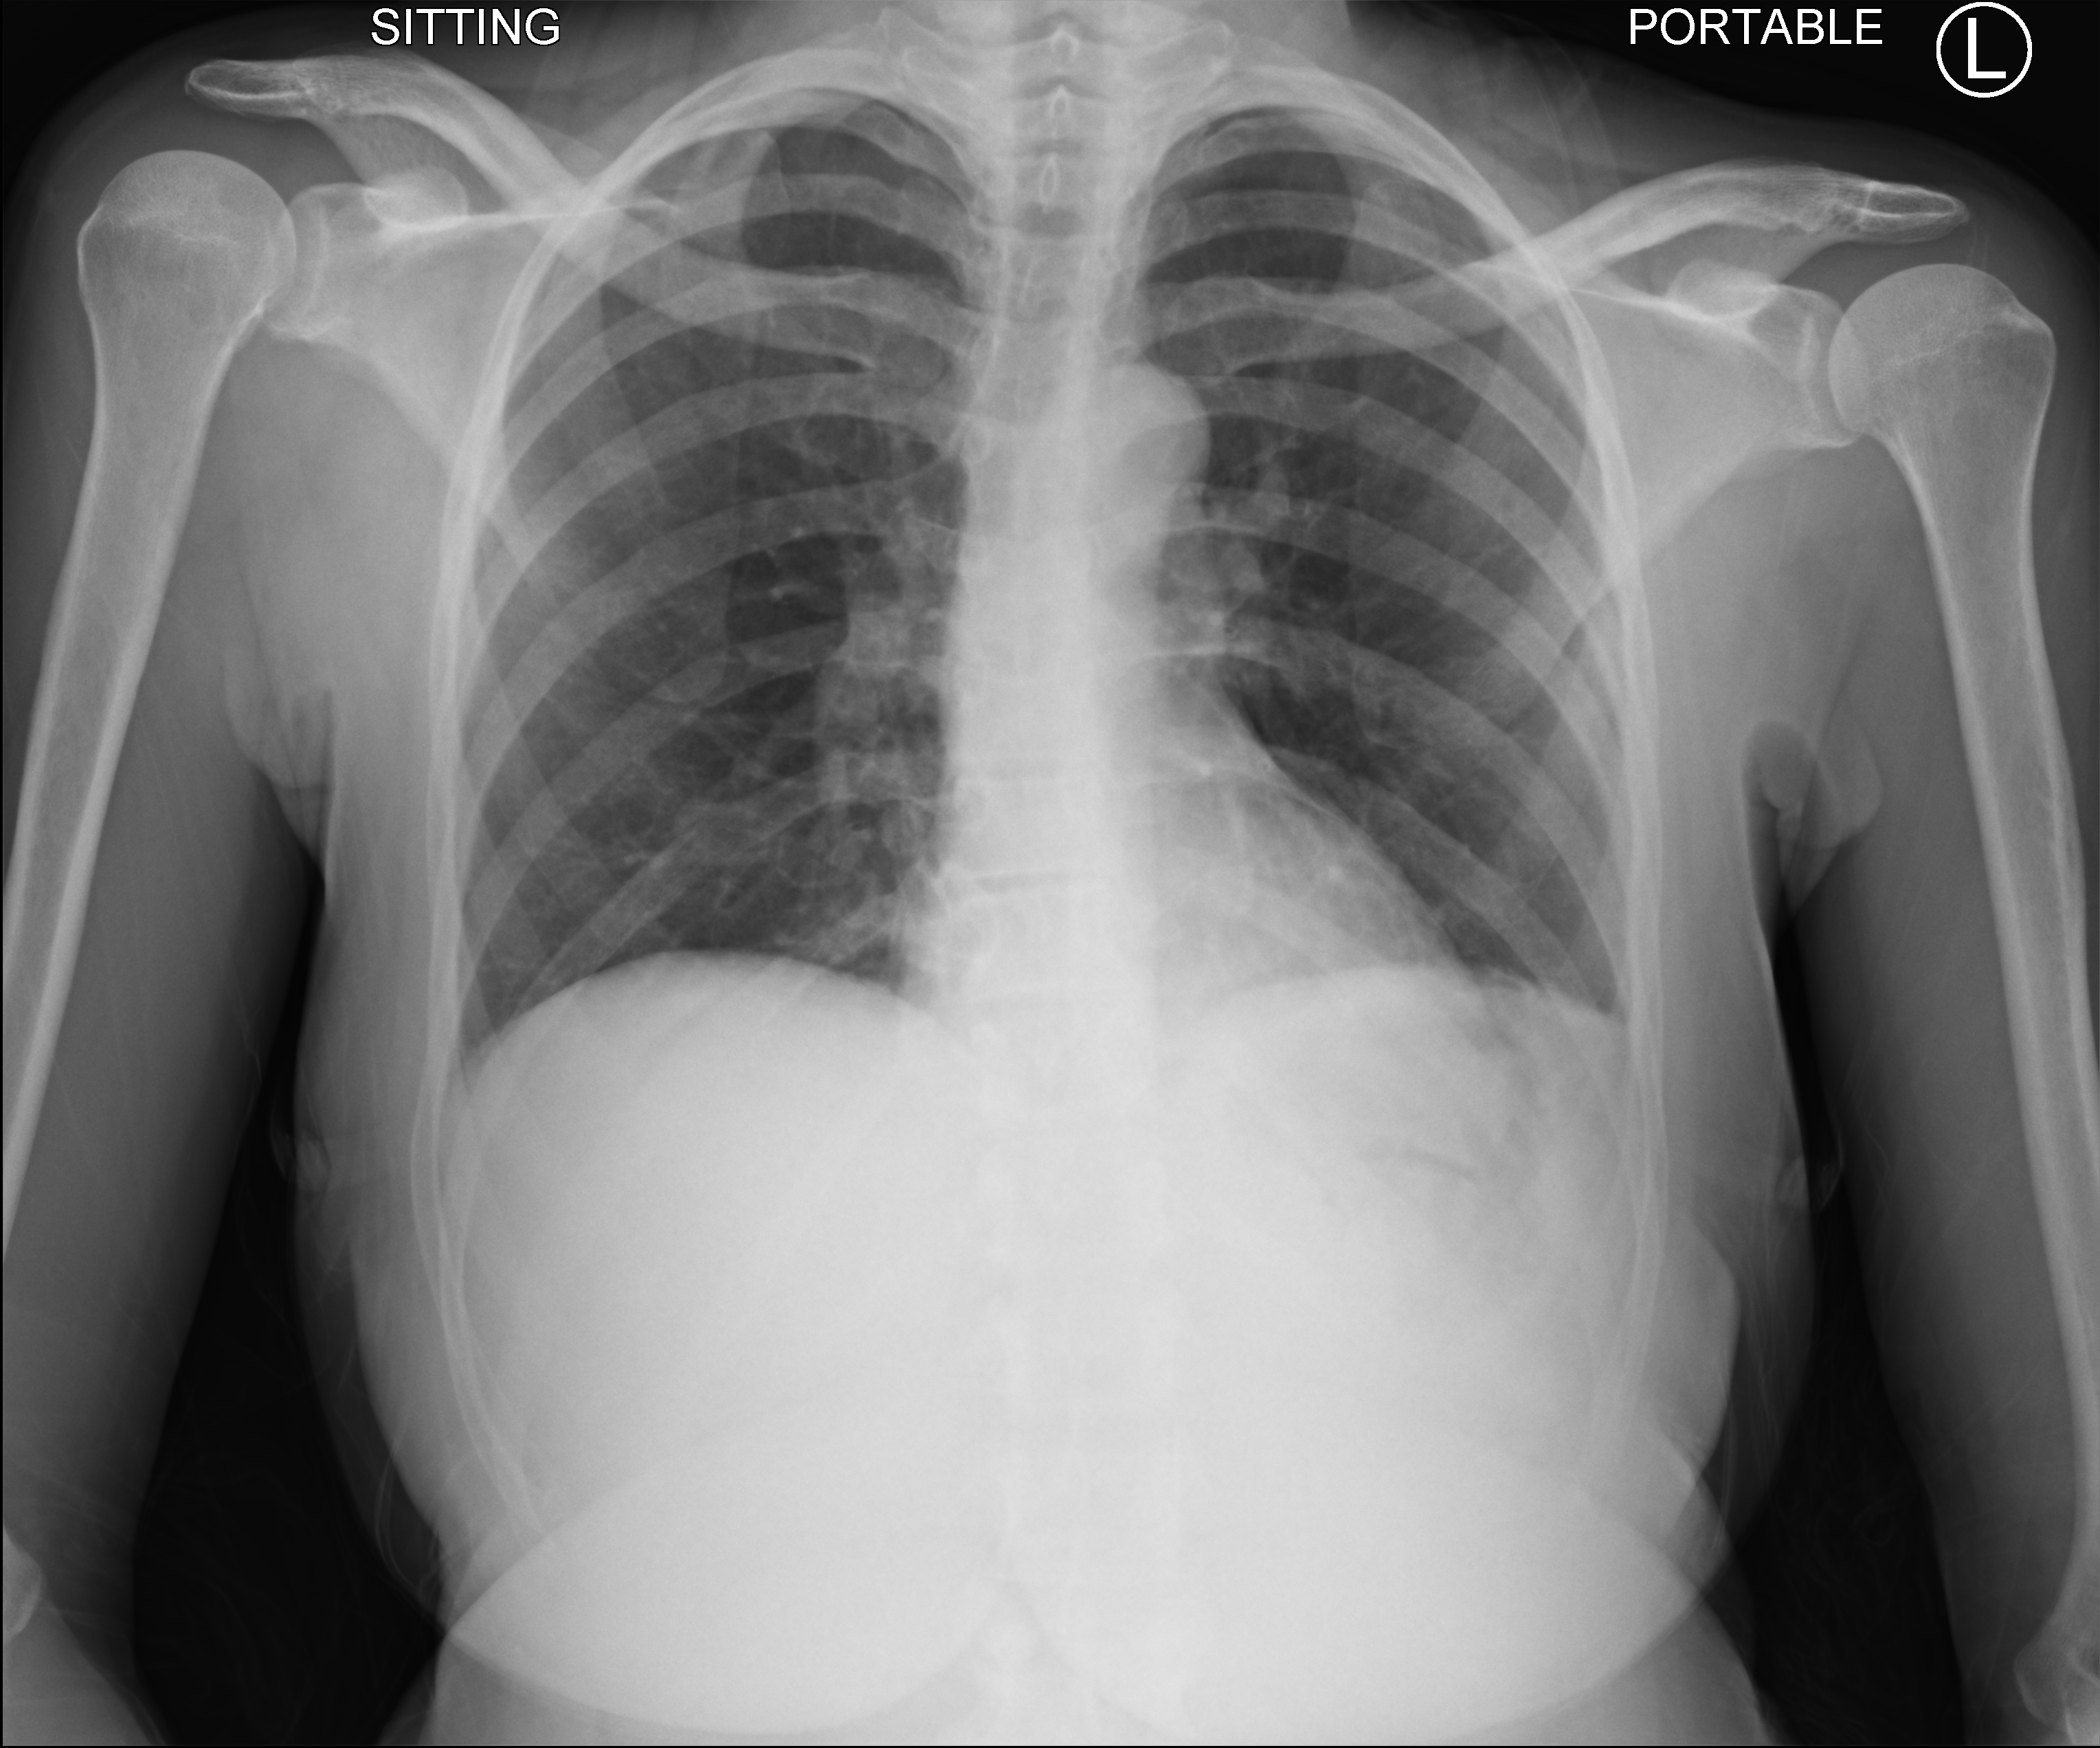
Bedside chest radiograph (computed radiography), anteroposterior (AP) projection. Patient hospitalised with COVID-19; female, aged 18–59 years.
Admission-level facts for this patient (not findings on this image; timing relative to this image not recorded): admitted to intensive care during this hospital stay: no; length of hospital stay: 1 day.